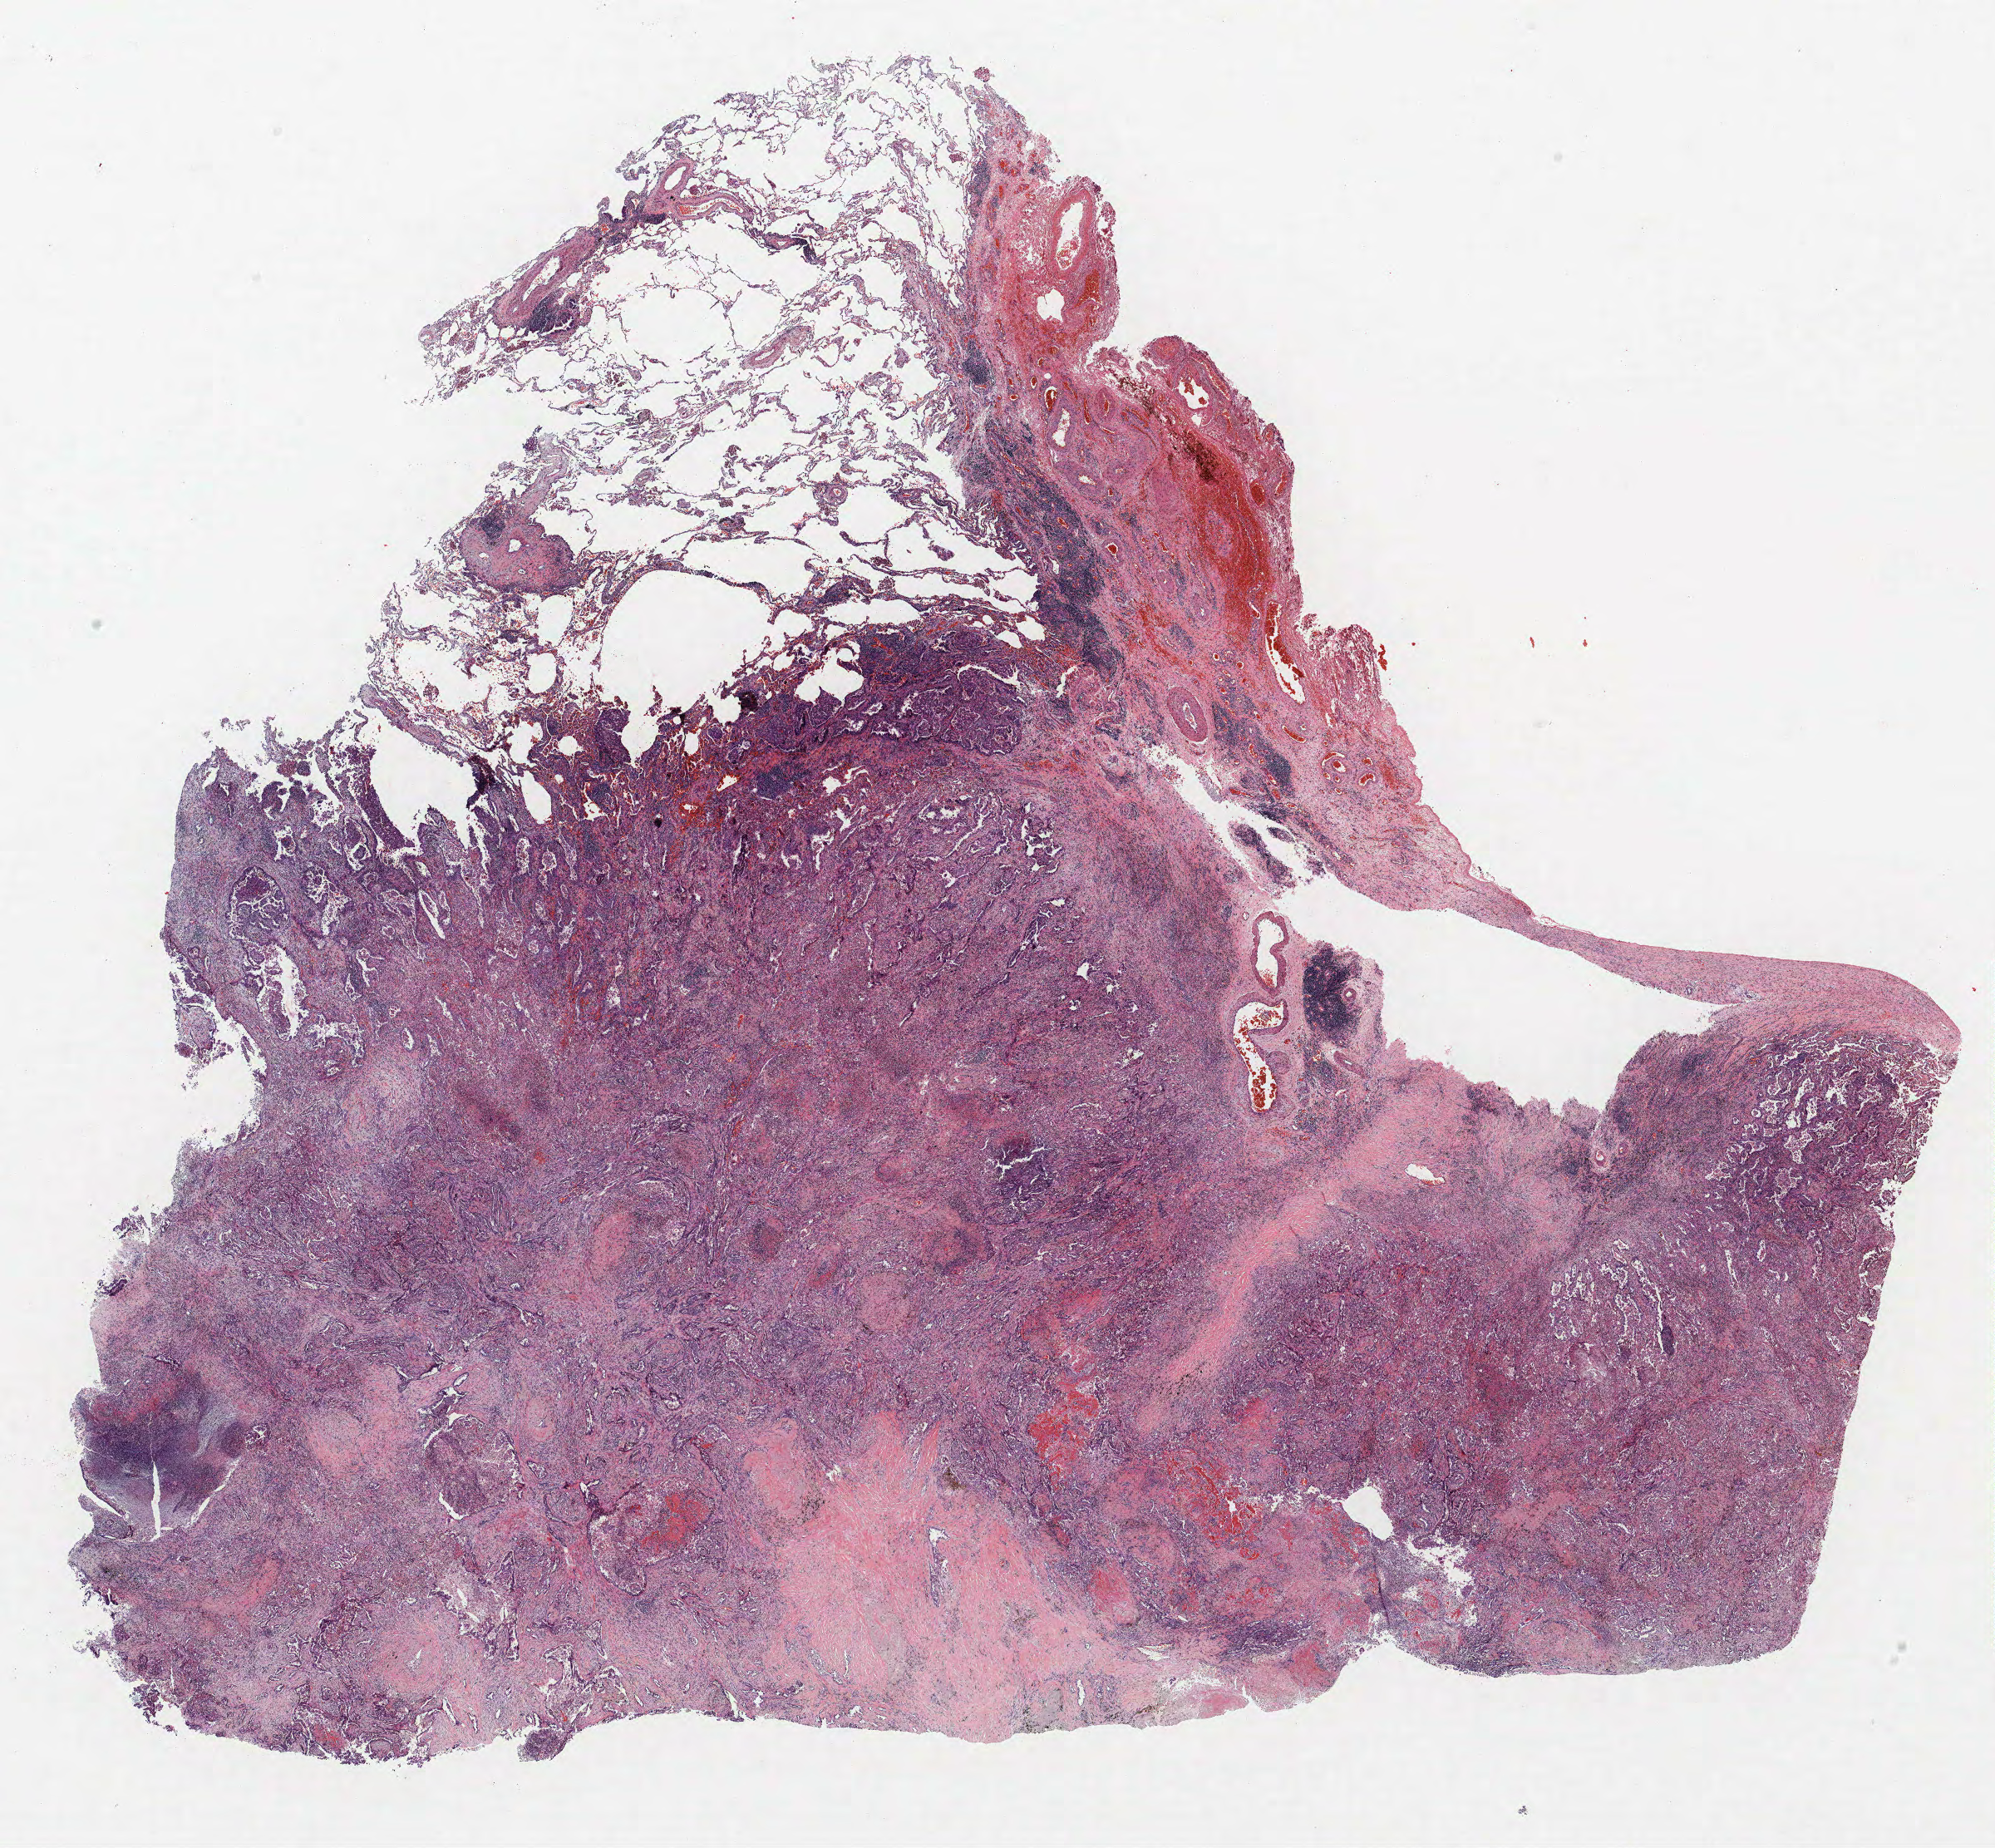
Hematoxylin and eosin (H&E) stained whole-slide image, low-resolution overview of the scanned area, about 19.2 x 17.8 mm (slide scanned at 40x). Formalin-fixed paraffin-embedded (FFPE) section. Lung. Male patient, aged 71 at enrolment. Current smoker at enrolment. Grade: moderately differentiated (G2).
* ICD-O-3 topography: upper lobe of lung (C34.1)
* tumour size (pathology): 35 mm
* primary tumour location (clinical record): left upper lobe
* stage (AJCC 6th edition): IIB
* participant's lung-cancer diagnosis: Bronchiolo-alveolar adenocarcinoma, NOS (ICD-O-3 8250/3)